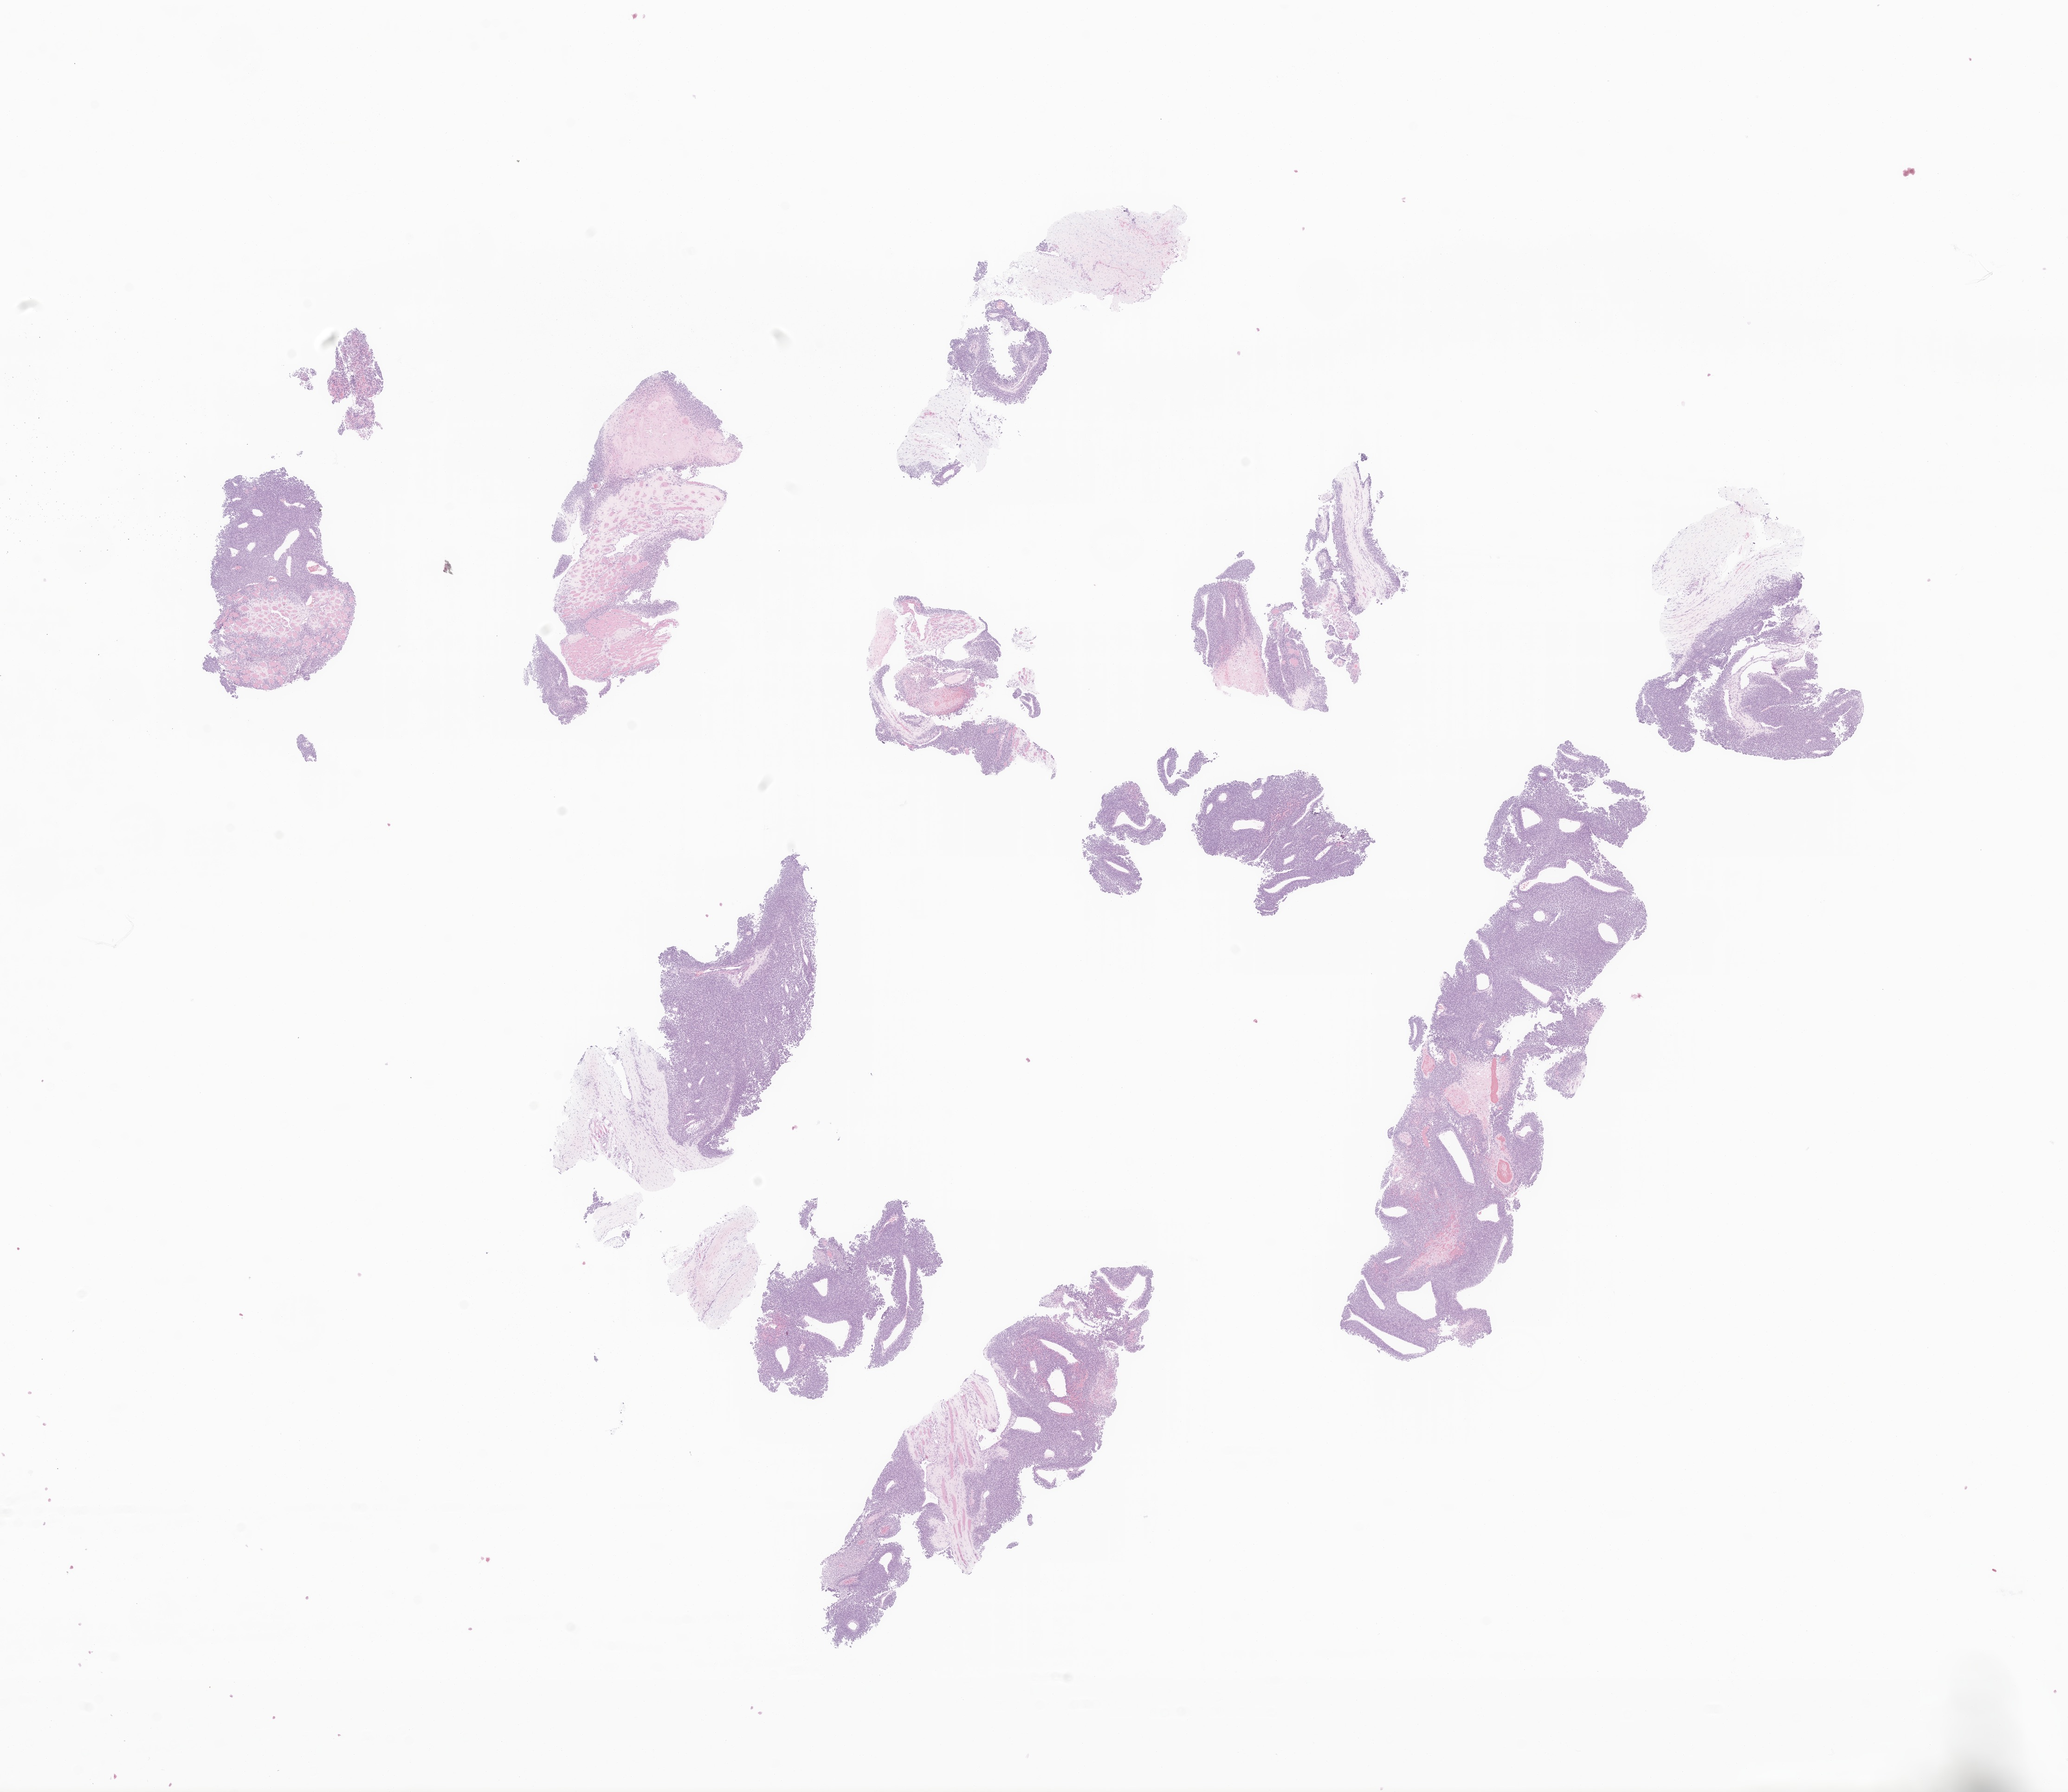
Hematoxylin and eosin (H&E) whole-slide image of tumor tissue from the soft tissue of lower extremity — a low-resolution overview of the entire scanned area, about 18.8 x 16.3 mm; FFPE section. Patient: male, age 152 months (12 years 8 months).
Diagnosis: Ewing sarcoma.